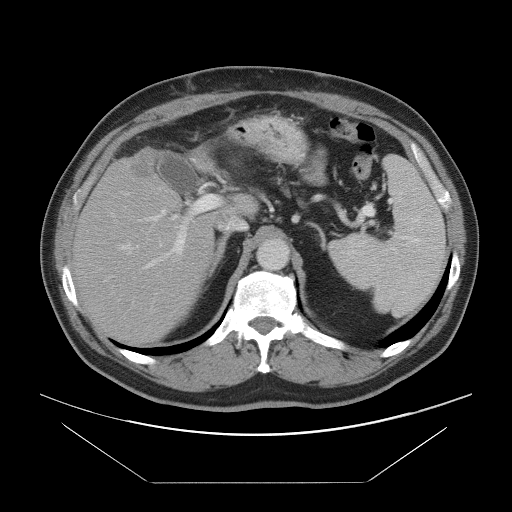
Contrast-enhanced abdominal CT, one axial slice; position 58 of 97 along the scan axis; 120 kVp; intravenous contrast given; soft-tissue window (W 400 / L 40 HU); 5 mm slice thickness; 512 × 512 image matrix. Male patient, age 62 years. Case-level facts recorded for this patient, not image findings: diagnosis: colorectal cancer liver metastases, imaged before liver resection; multiple liver metastases: no; largest metastasis: 7 cm; disease in both lobes: yes.
Outlined on this slice (expert manual segmentation):
- hepatic veins: bounding box [x1, y1, x2, y2] px = [120, 187, 167, 254]
- liver: [75, 149, 249, 343]
- planned liver remnant (the part of the liver to remain after resection): [75, 176, 221, 343]
- portal vein (with intrahepatic branches): [126, 193, 220, 271]
- liver metastasis: [130, 153, 154, 179]